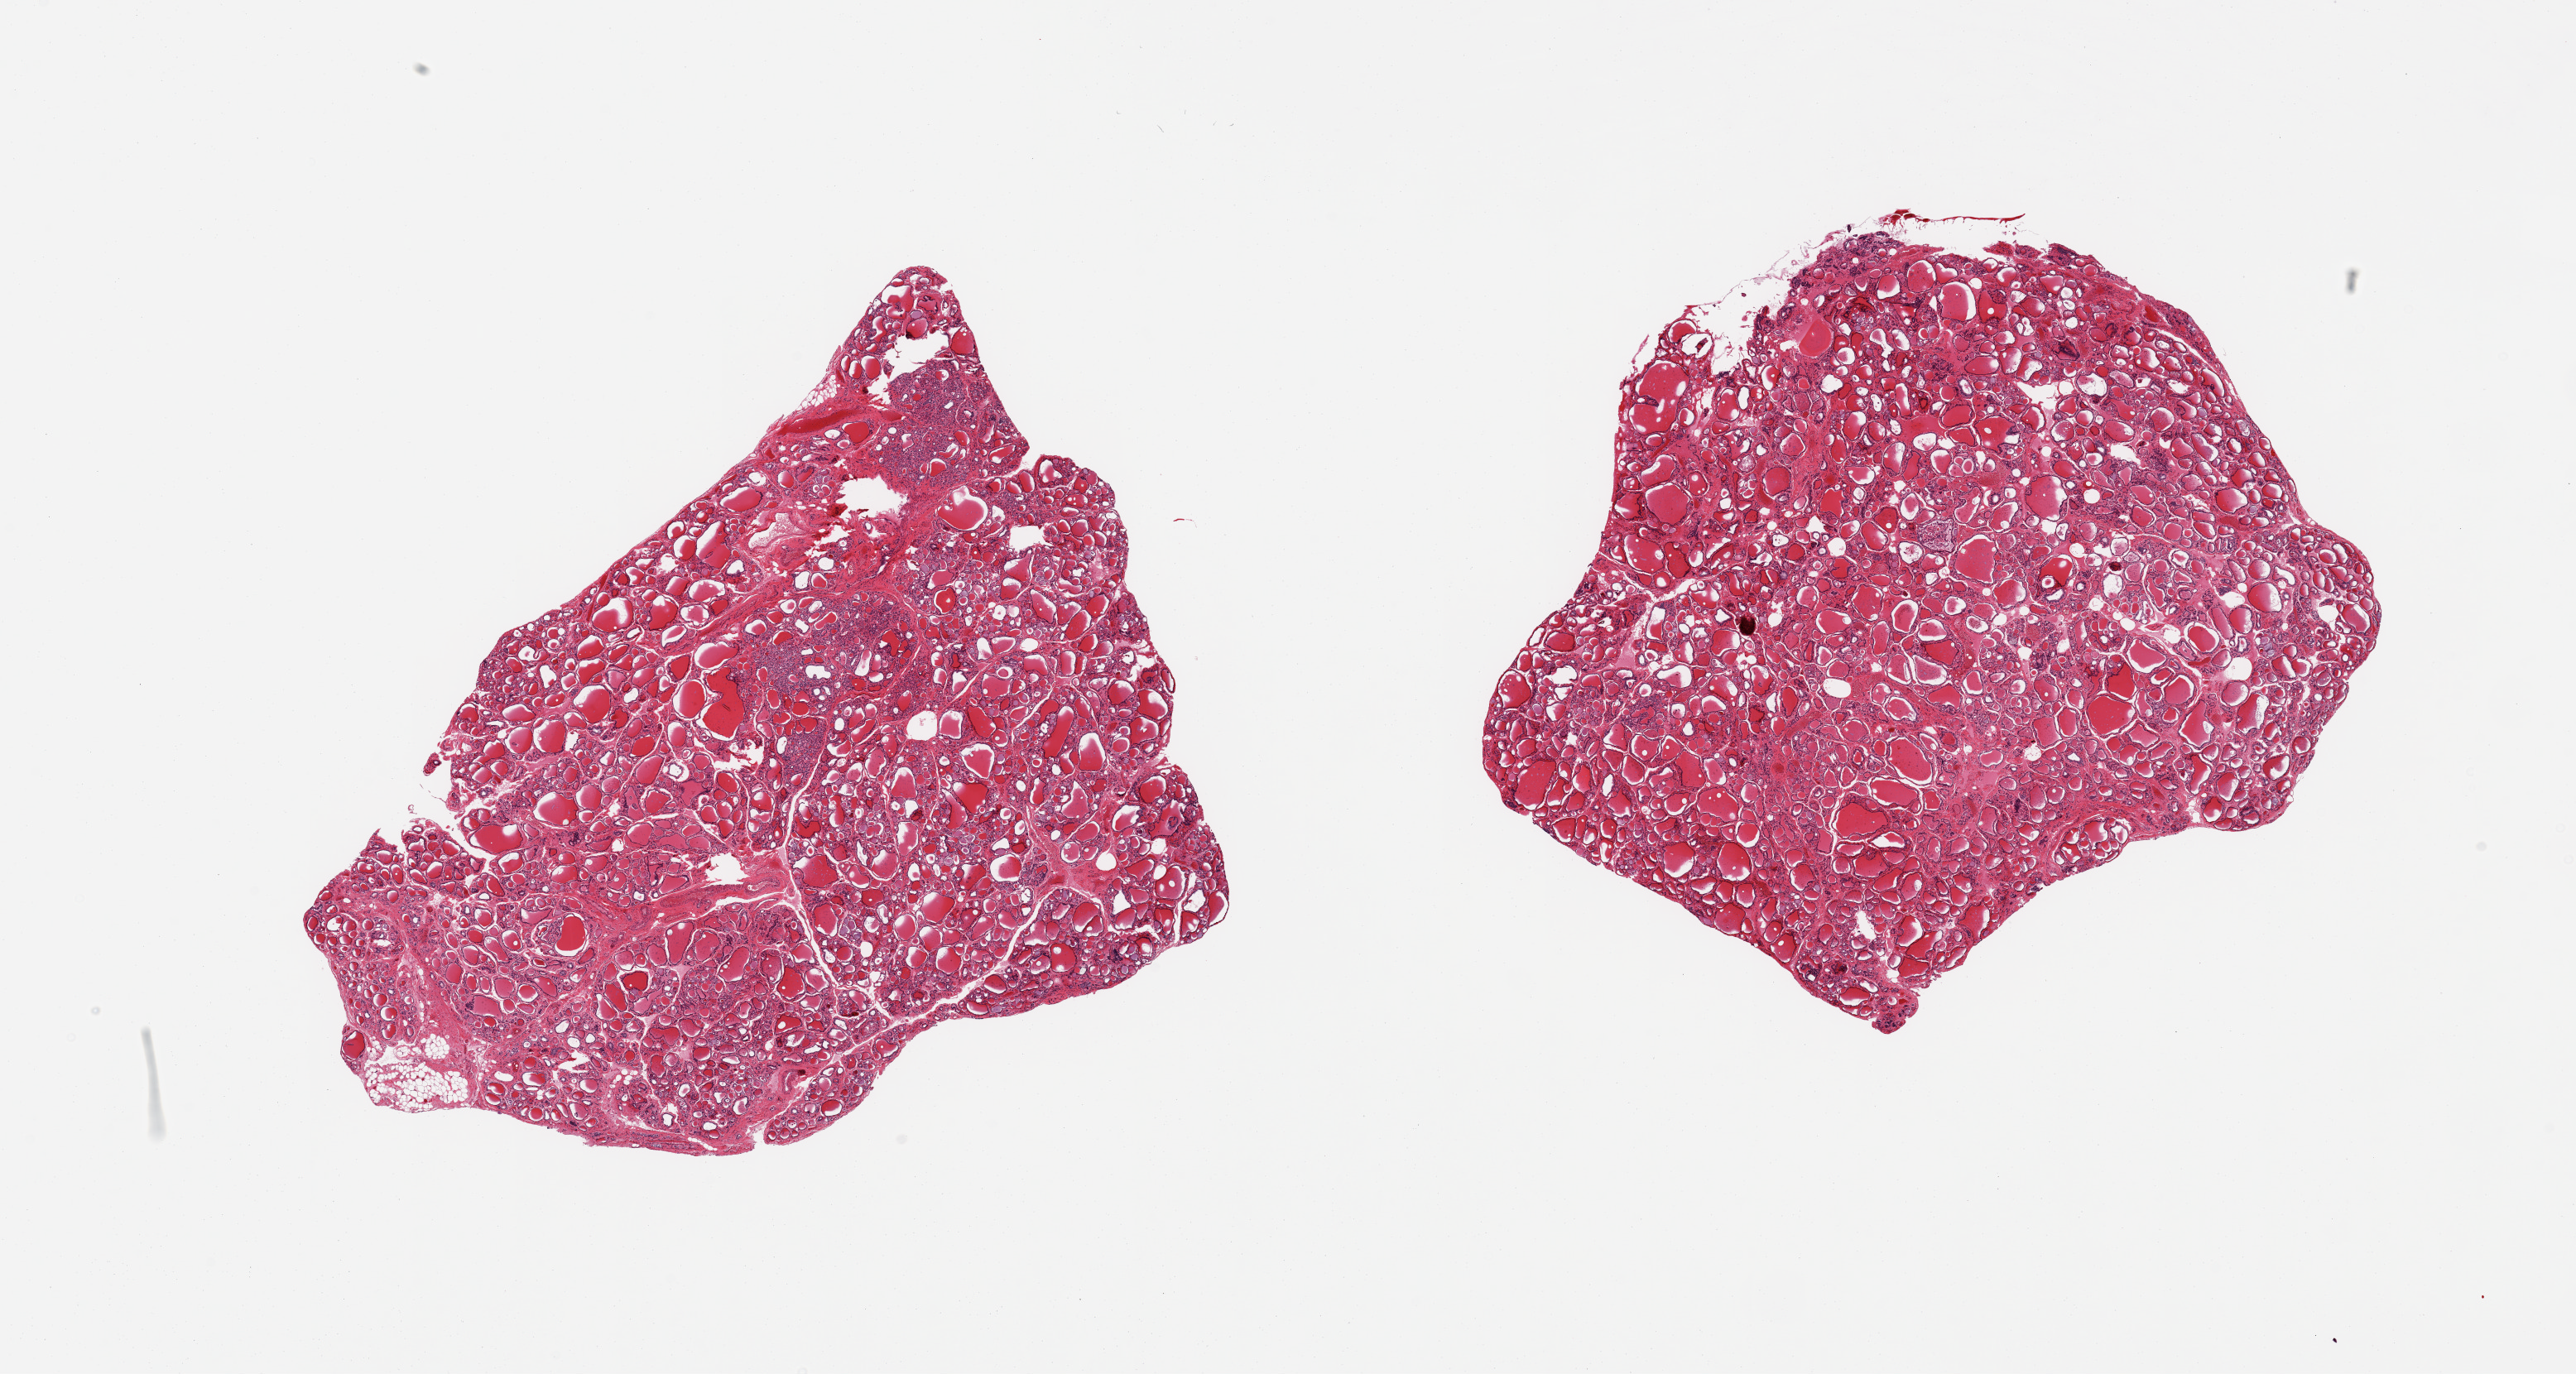
Hematoxylin and eosin (H&E) whole-slide image — whole scanned area (about 24.6 x 13.1 mm) shown as a low-resolution overview. PAXgene-fixed, paraffin-embedded tissue. Sampled site (target tissue): thyroid. Donor tissue sample.
• reviewer comment on this tissue sample: 2 pieces; well dissected